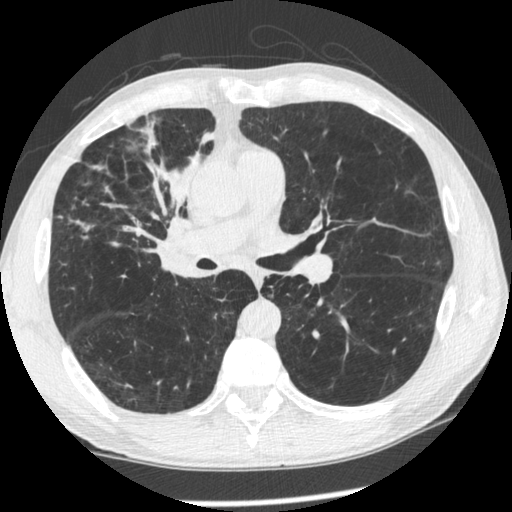
Low-dose screening chest CT, one axial slice. Position 132 of 261 along the scan axis. Reconstruction kernel STANDARD. Lung window (W 1500 / L -600 HU). 1.25 mm slice thickness. 512 × 512 image matrix, field of view 340 × 340 mm.
Outlined on this slice (expert manual segmentation):
- lesion 1 (tumor, upper lobe of right lung): box from (x=98, y=133) to (x=214, y=237) px